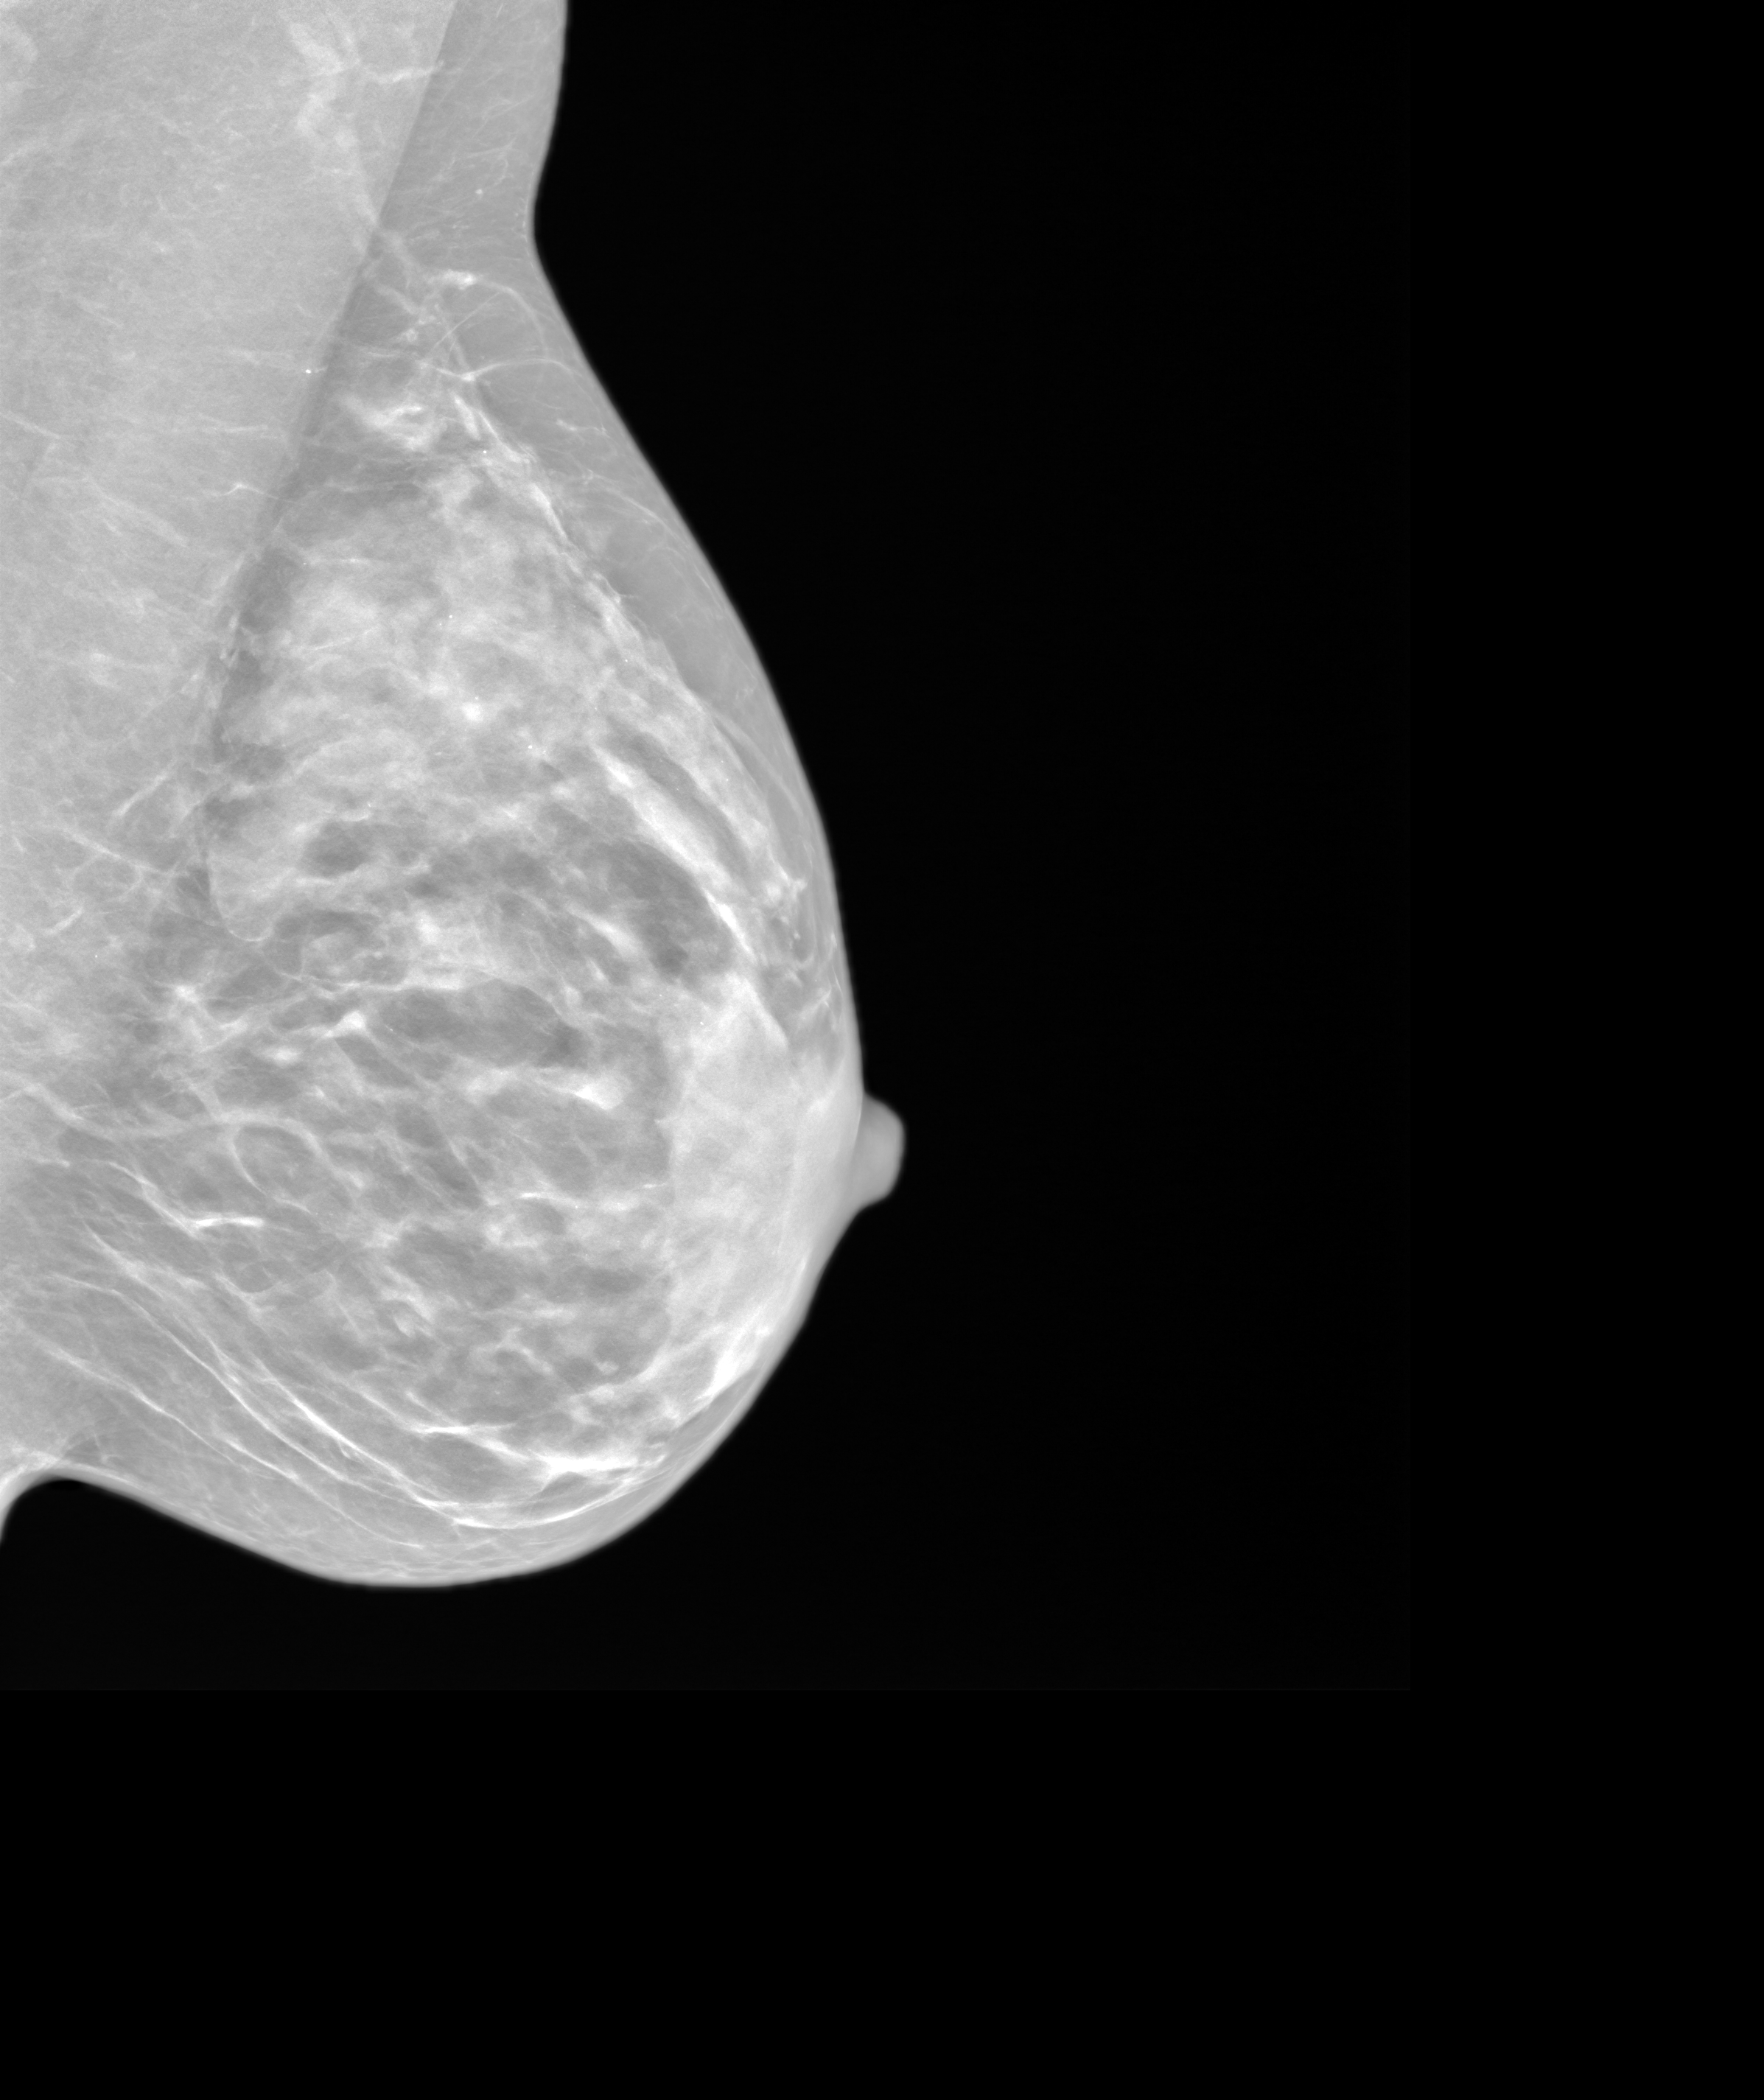
Synthesized 2-D mammogram reconstructed from digital breast tomosynthesis, left breast, medio-lateral oblique projection, annual screening mammography examination. Patient: female, 47 years.
Breast density at the screening exam (both breasts): heterogeneously dense (BI-RADS density category c). Final BI-RADS assessment for this screening round (tomosynthesis exam, both breasts): category 3. Recall: recalled for additional imaging after this screen.